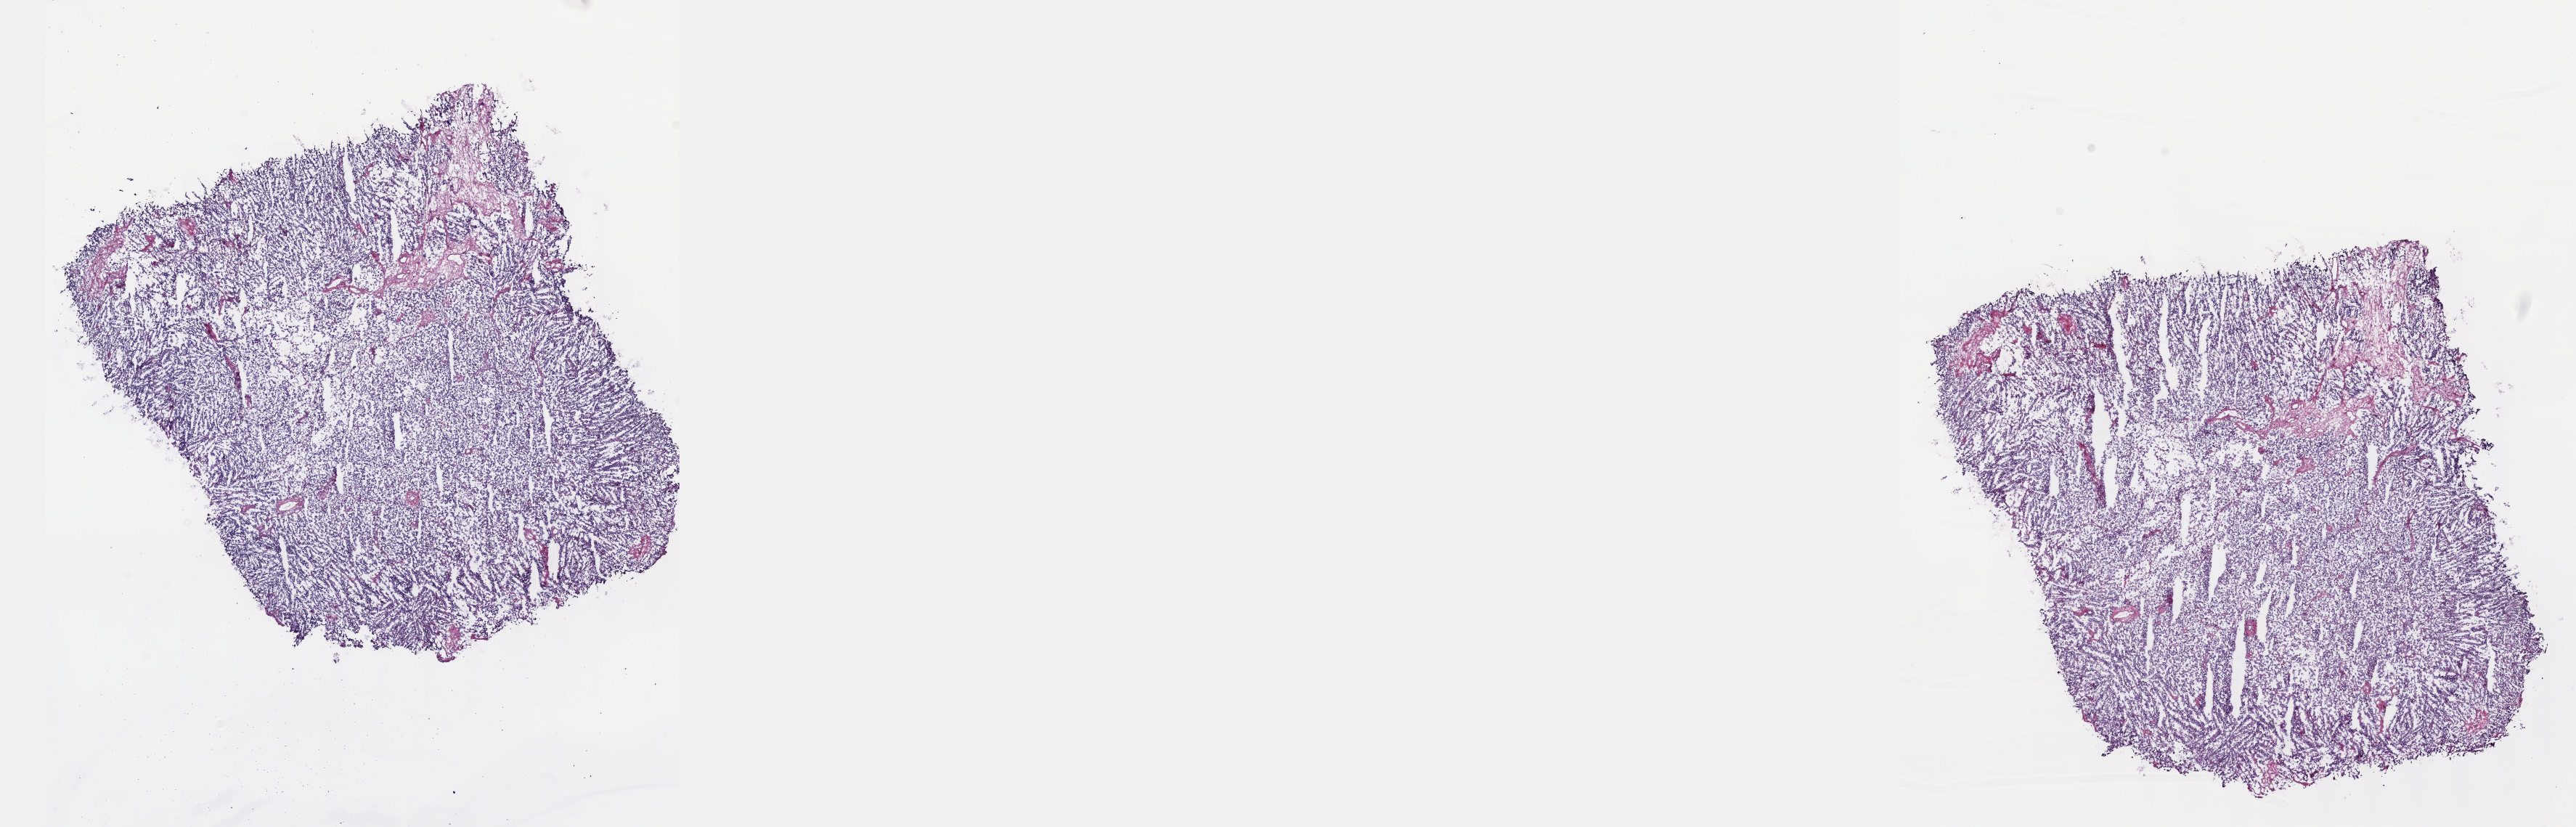
Hematoxylin and eosin (H&E) stained whole-slide image — shown as a low-resolution overview of the whole scanned area (about 28.7 x 9.2 mm, slide scanned at 40x), frozen section, sample: primary tumour, testis. Male, age 45 years at initial diagnosis. Pathologist review of this section (percent, as recorded): tumour cells 100%, tumour nuclei 70%.
Pathologic diagnosis: Seminoma, NOS.